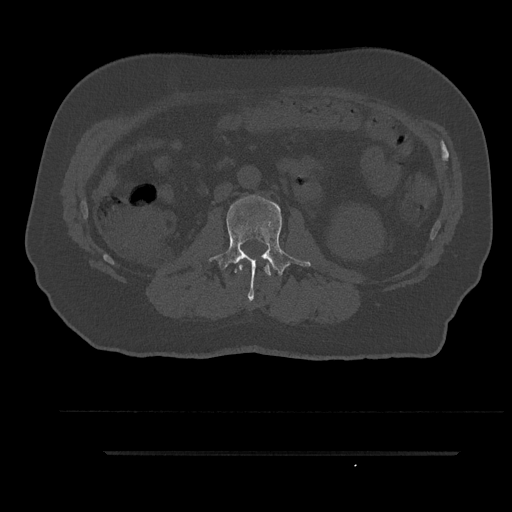
CT including the spine, one axial slice; slice 112 of 797 in the series (ordered by position); 120 kVp; bone window (W 1800 / L 400 HU); 0.5 mm slice thickness; 512 × 512 image matrix, field of view 432 × 432 mm. Patient: male, 63 years. Case-level facts recorded for this patient, not image findings: primary cancer: renal.
Annotated regions visible in this slice (semi-automatic segmentation, software-assisted and operator-edited):
- L1 vertebra: bounding box (x1, y1, x2, y2) in pixels: (239, 264, 271, 276)
- L2 vertebra: (208, 196, 311, 301)